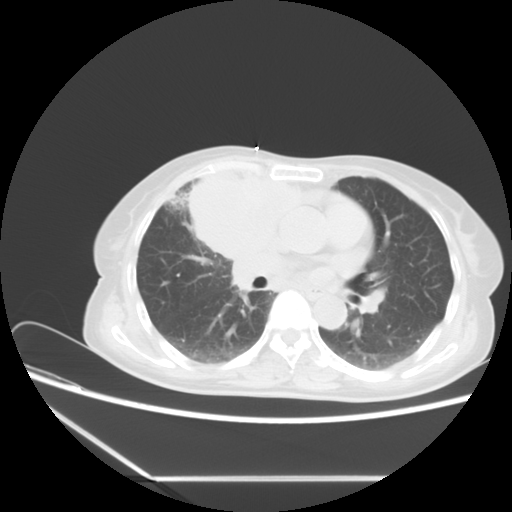
Chest CT, one axial slice; slice 7 of 16 in the series (ordered by position); reconstruction kernel STANDARD; 120 kVp; lung window (W 1500 / L -600 HU); 512 × 512 image matrix. Patient: female, 63 years. From the clinical record (not read from this slice): clinical TNM (as recorded): T2b N1 M0.
Outlined on this slice (bounding box drawn by a radiologist):
- lung tumour (recorded histology: adenocarcinoma): bounding box [x1, y1, x2, y2] px = [184, 162, 308, 263]